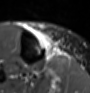
MRI of an extremity soft-tissue mass, one axial slice; slice 20 of 60 in the series (ordered by position); STIR; MR volume resampled by the dataset authors to the PET/CT grid (not the native acquisition matrix); 3.27 mm slice thickness; 90 × 93 image matrix, field of view 88 × 91 mm. Female patient. Case-level facts recorded for this patient, not image findings: histological type: undifferentiated – high grade; grade: high; site of the primary tumour: right thigh.
Outlined on this slice (expert contour drawn on MRI and transferred to this co-registered scan by the dataset authors):
- gross tumour volume (mass): box from (x=35, y=30) to (x=59, y=59) px